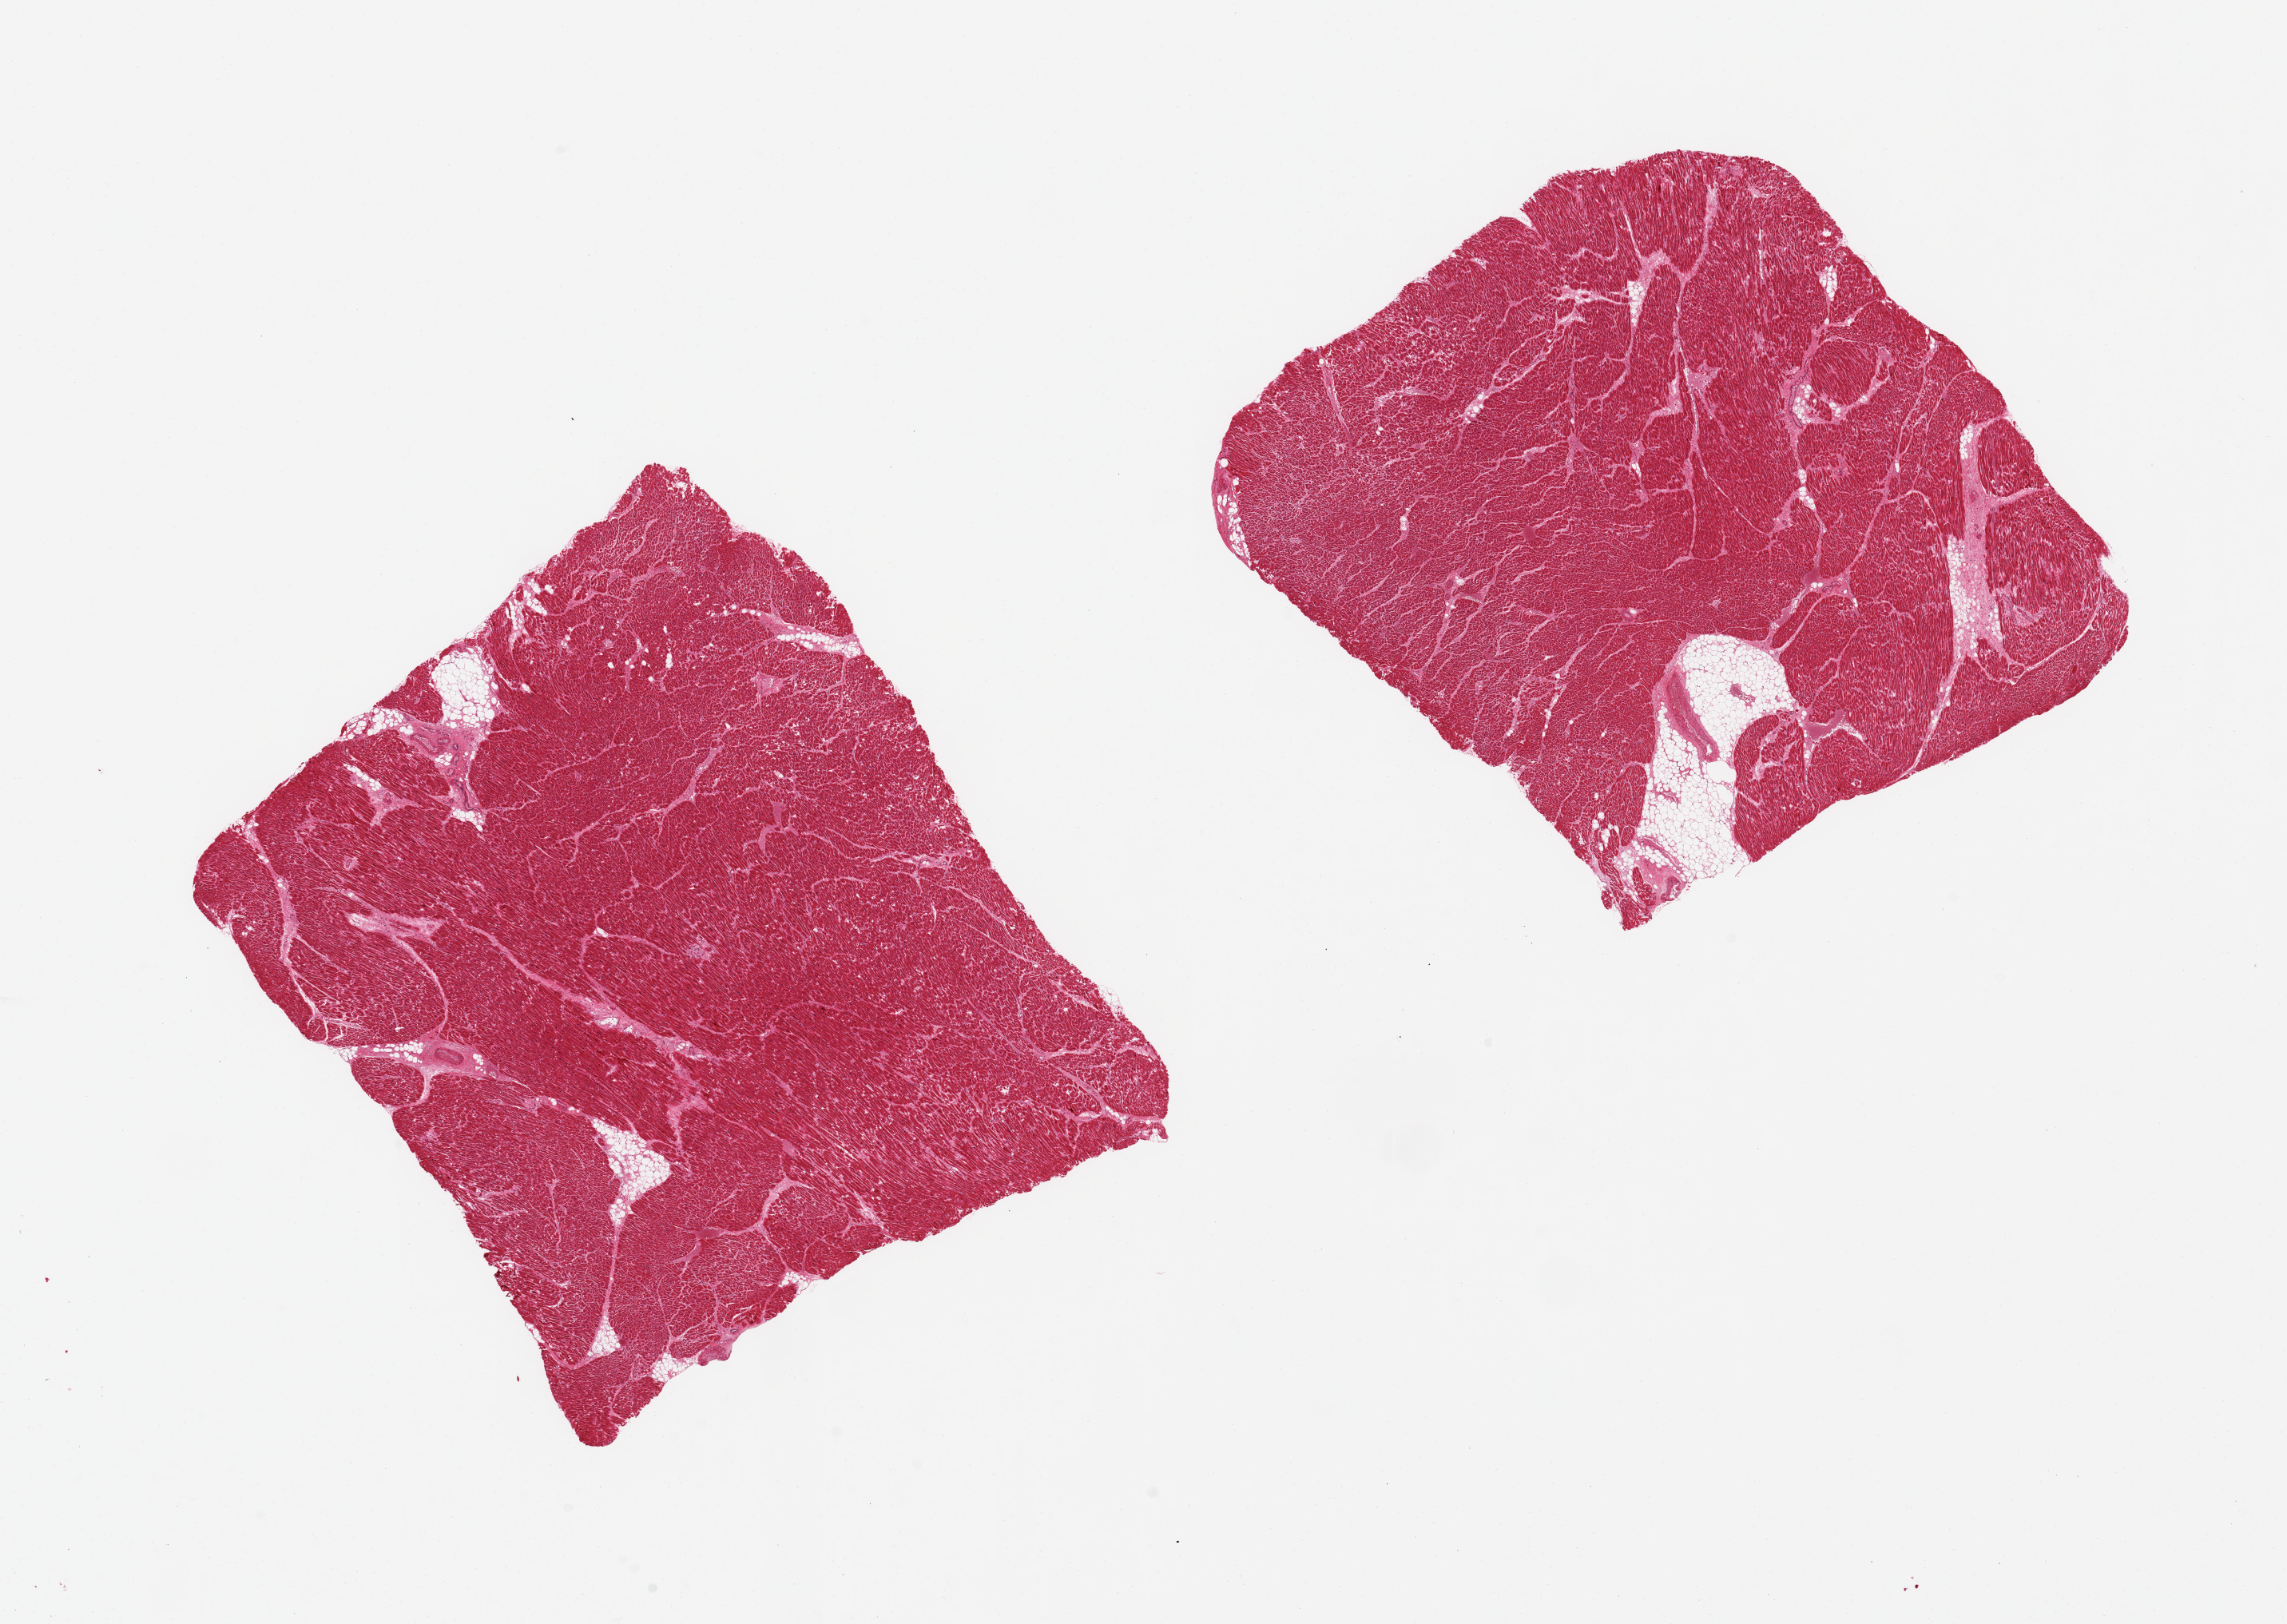
Hematoxylin and eosin (H&E) whole-slide image — whole scanned area (about 22.6 x 16.1 mm) shown as a low-resolution overview. PAXgene-fixed, paraffin-embedded tissue. Section of heart (target tissue). Tissue donor sample. Donor: male.
• review note (as recorded): 2 pieces ~7x6mm. Minimal interstitial fibrosis